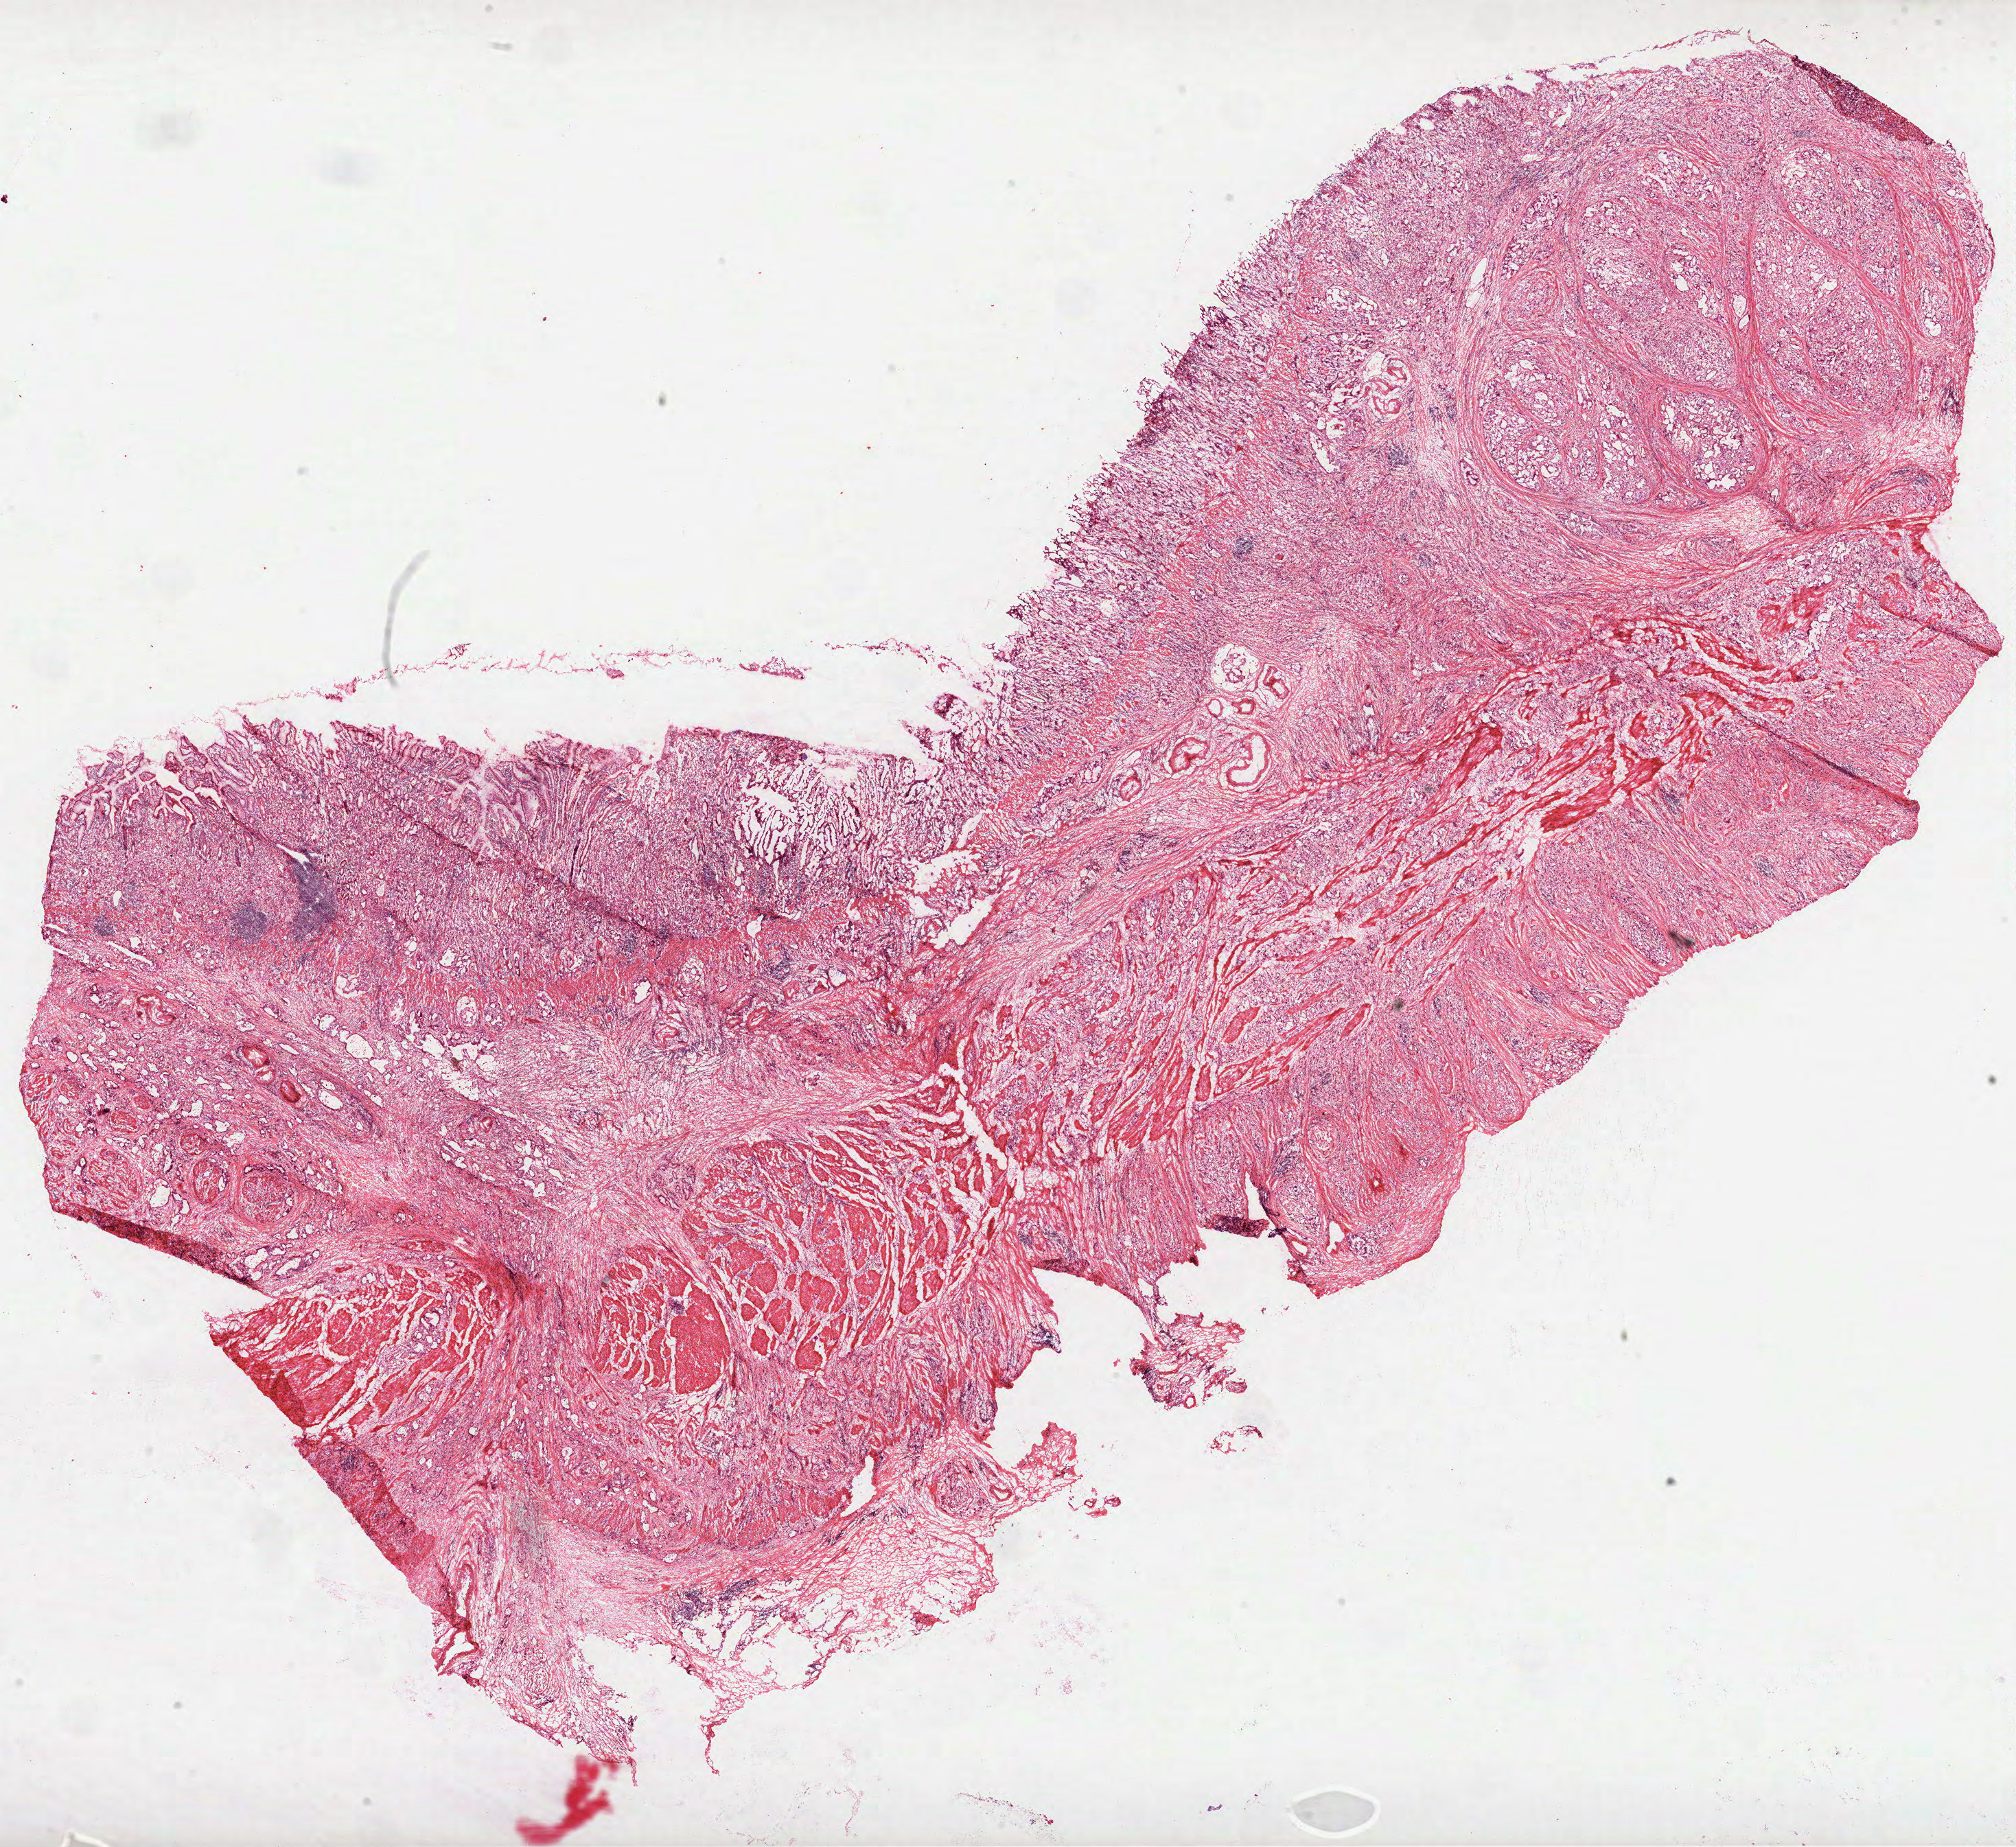
H&E-stained whole-slide image — a low-resolution overview of the entire scanned area, about 23.7 x 21.7 mm (slide scanned at 40x), frozen section, primary tumour sample from the stomach. Patient: male, age at initial diagnosis 62 years. Histologic grade: G3 (poorly differentiated). Composition of this section per pathologist review: tumour cells 62%, tumour nuclei 65%, normal cells 8%, stromal cells 30%, necrosis 0%.
• TNM: T4b N2 M0
• histologic diagnosis: Adenocarcinoma, NOS (fundus of stomach)
• AJCC pathologic stage: IIIC (7th edition)